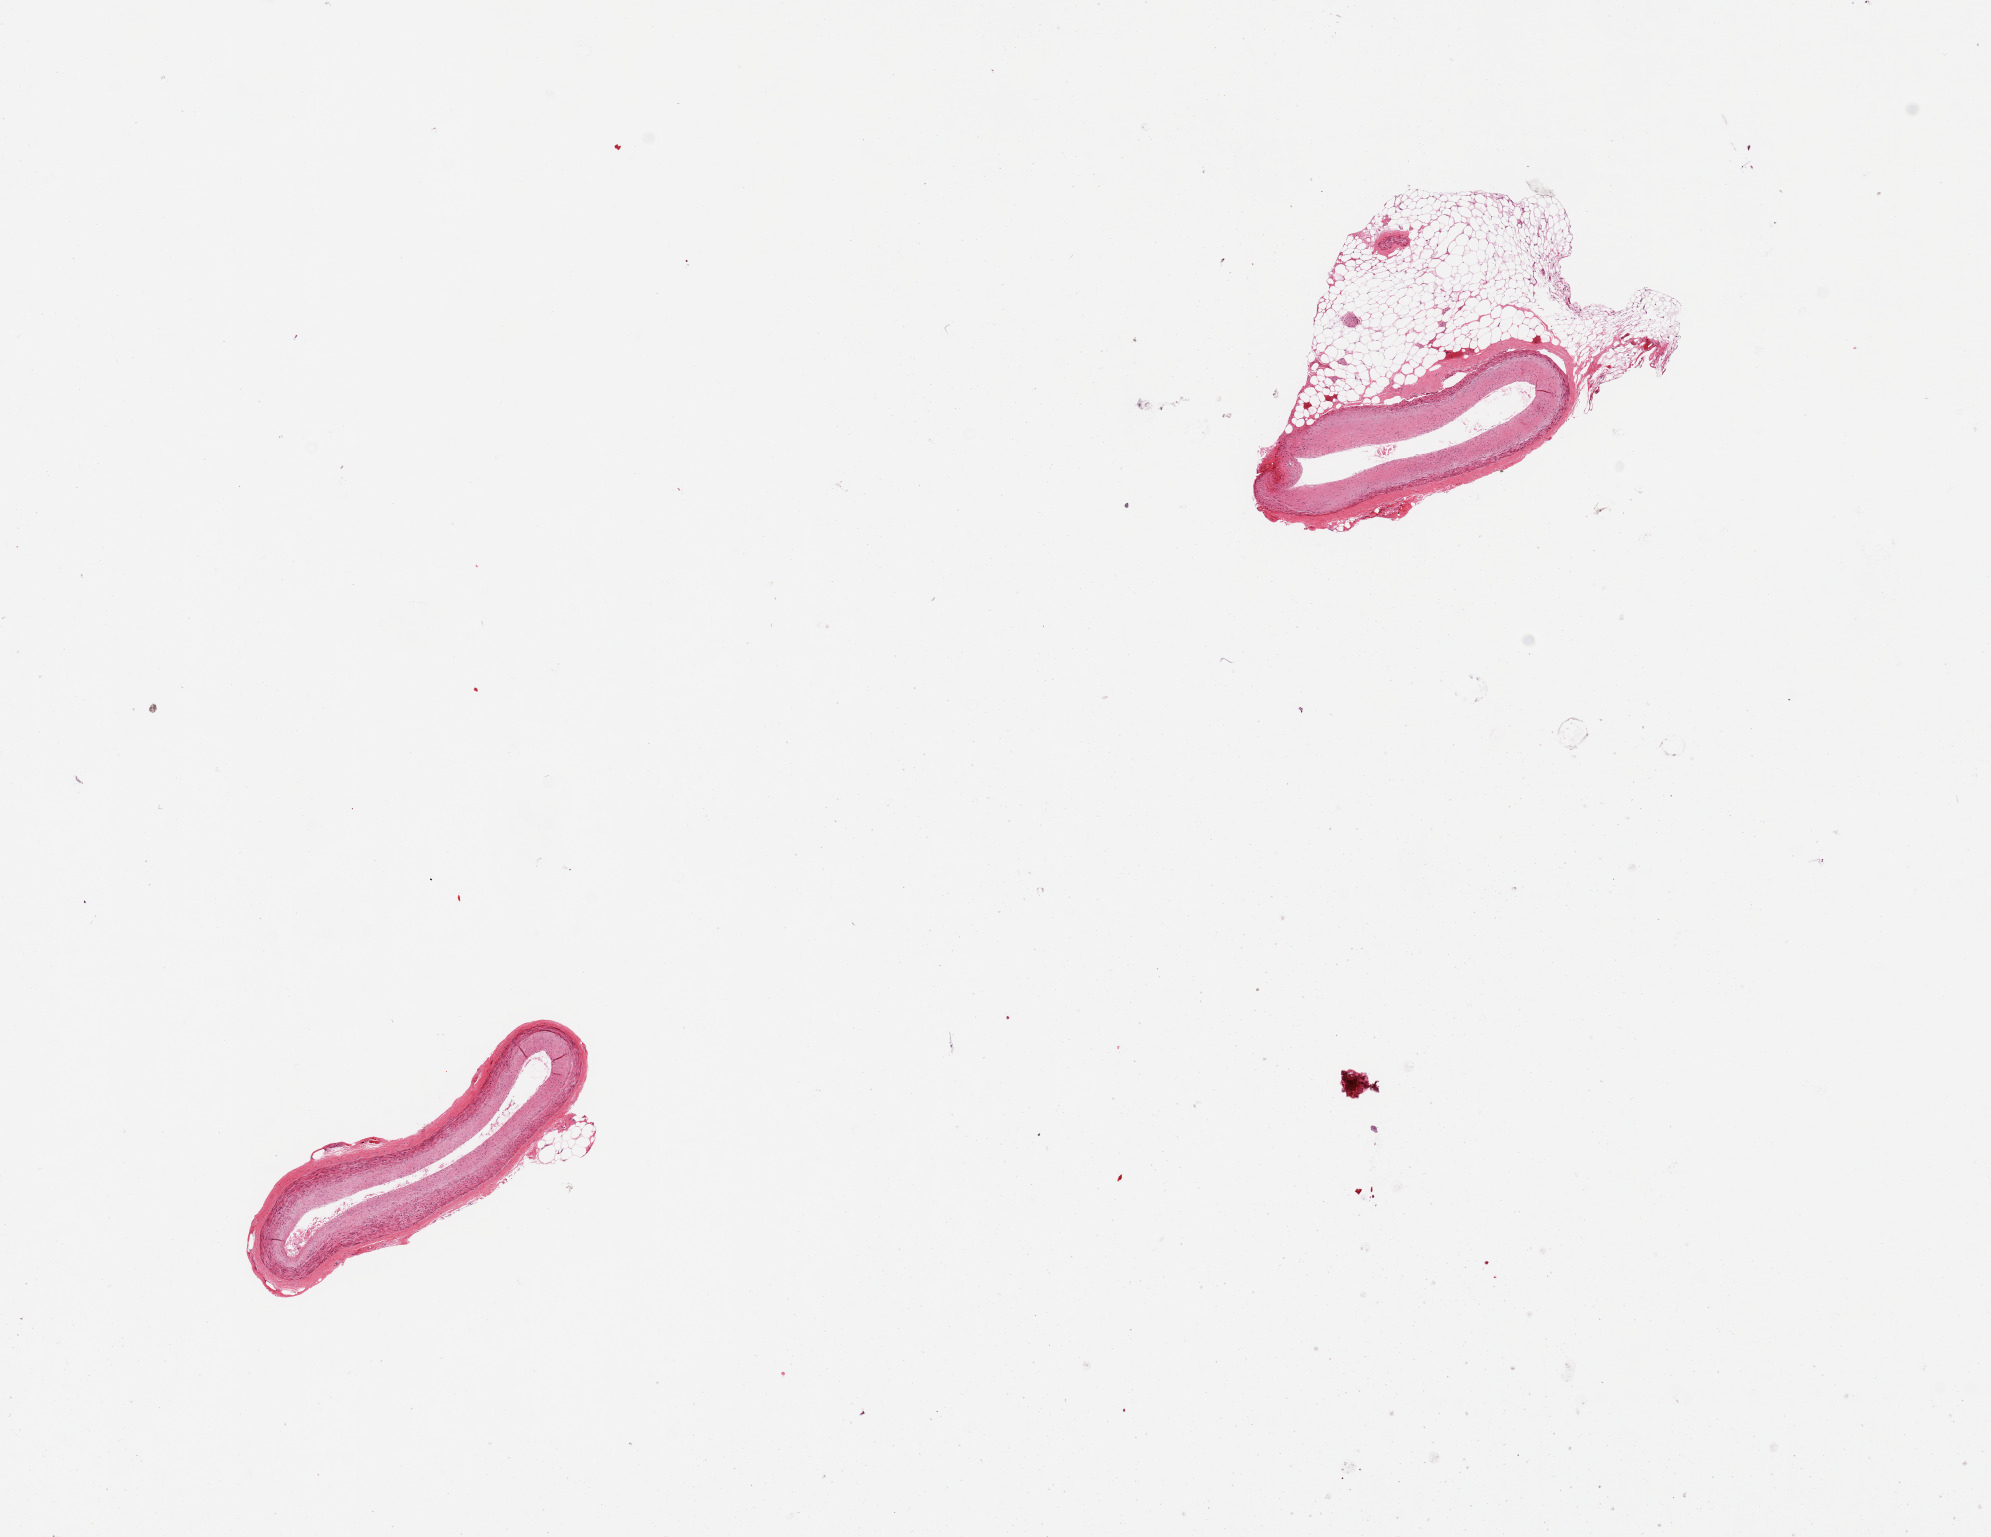
Haematoxylin and eosin whole-slide image, low-resolution overview of the scanned area, about 15.8 x 12.2 mm, PAXgene-fixed paraffin-embedded (PFPE) section, section of coronary artery (target tissue), tissue donor sample. Donor sex: female.
Review note (as recorded): 2 pieces, minimal atherosis, ~1.5mm nubbin fat attached to one.